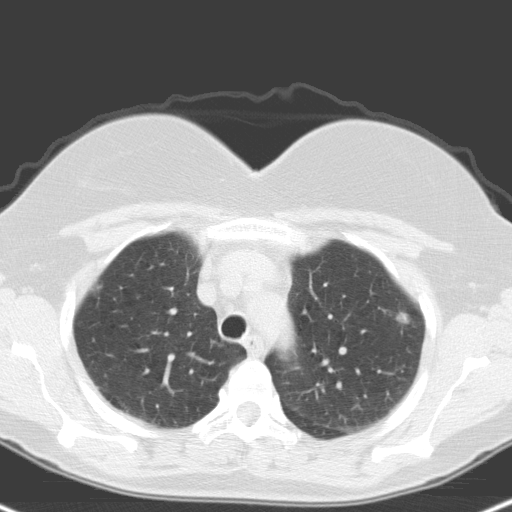
Low-dose screening chest CT, one axial slice; position 123 of 148 along the scan axis; 120 kVp; lung window (W 1500 / L -600 HU); 3.2 mm slice thickness; 512 × 512 image matrix, field of view 314 × 314 mm.
Structures marked on this image (manually delineated by an expert):
- lesion 1 (tumor, upper lobe of left lung): box from (x=396, y=312) to (x=409, y=333) px